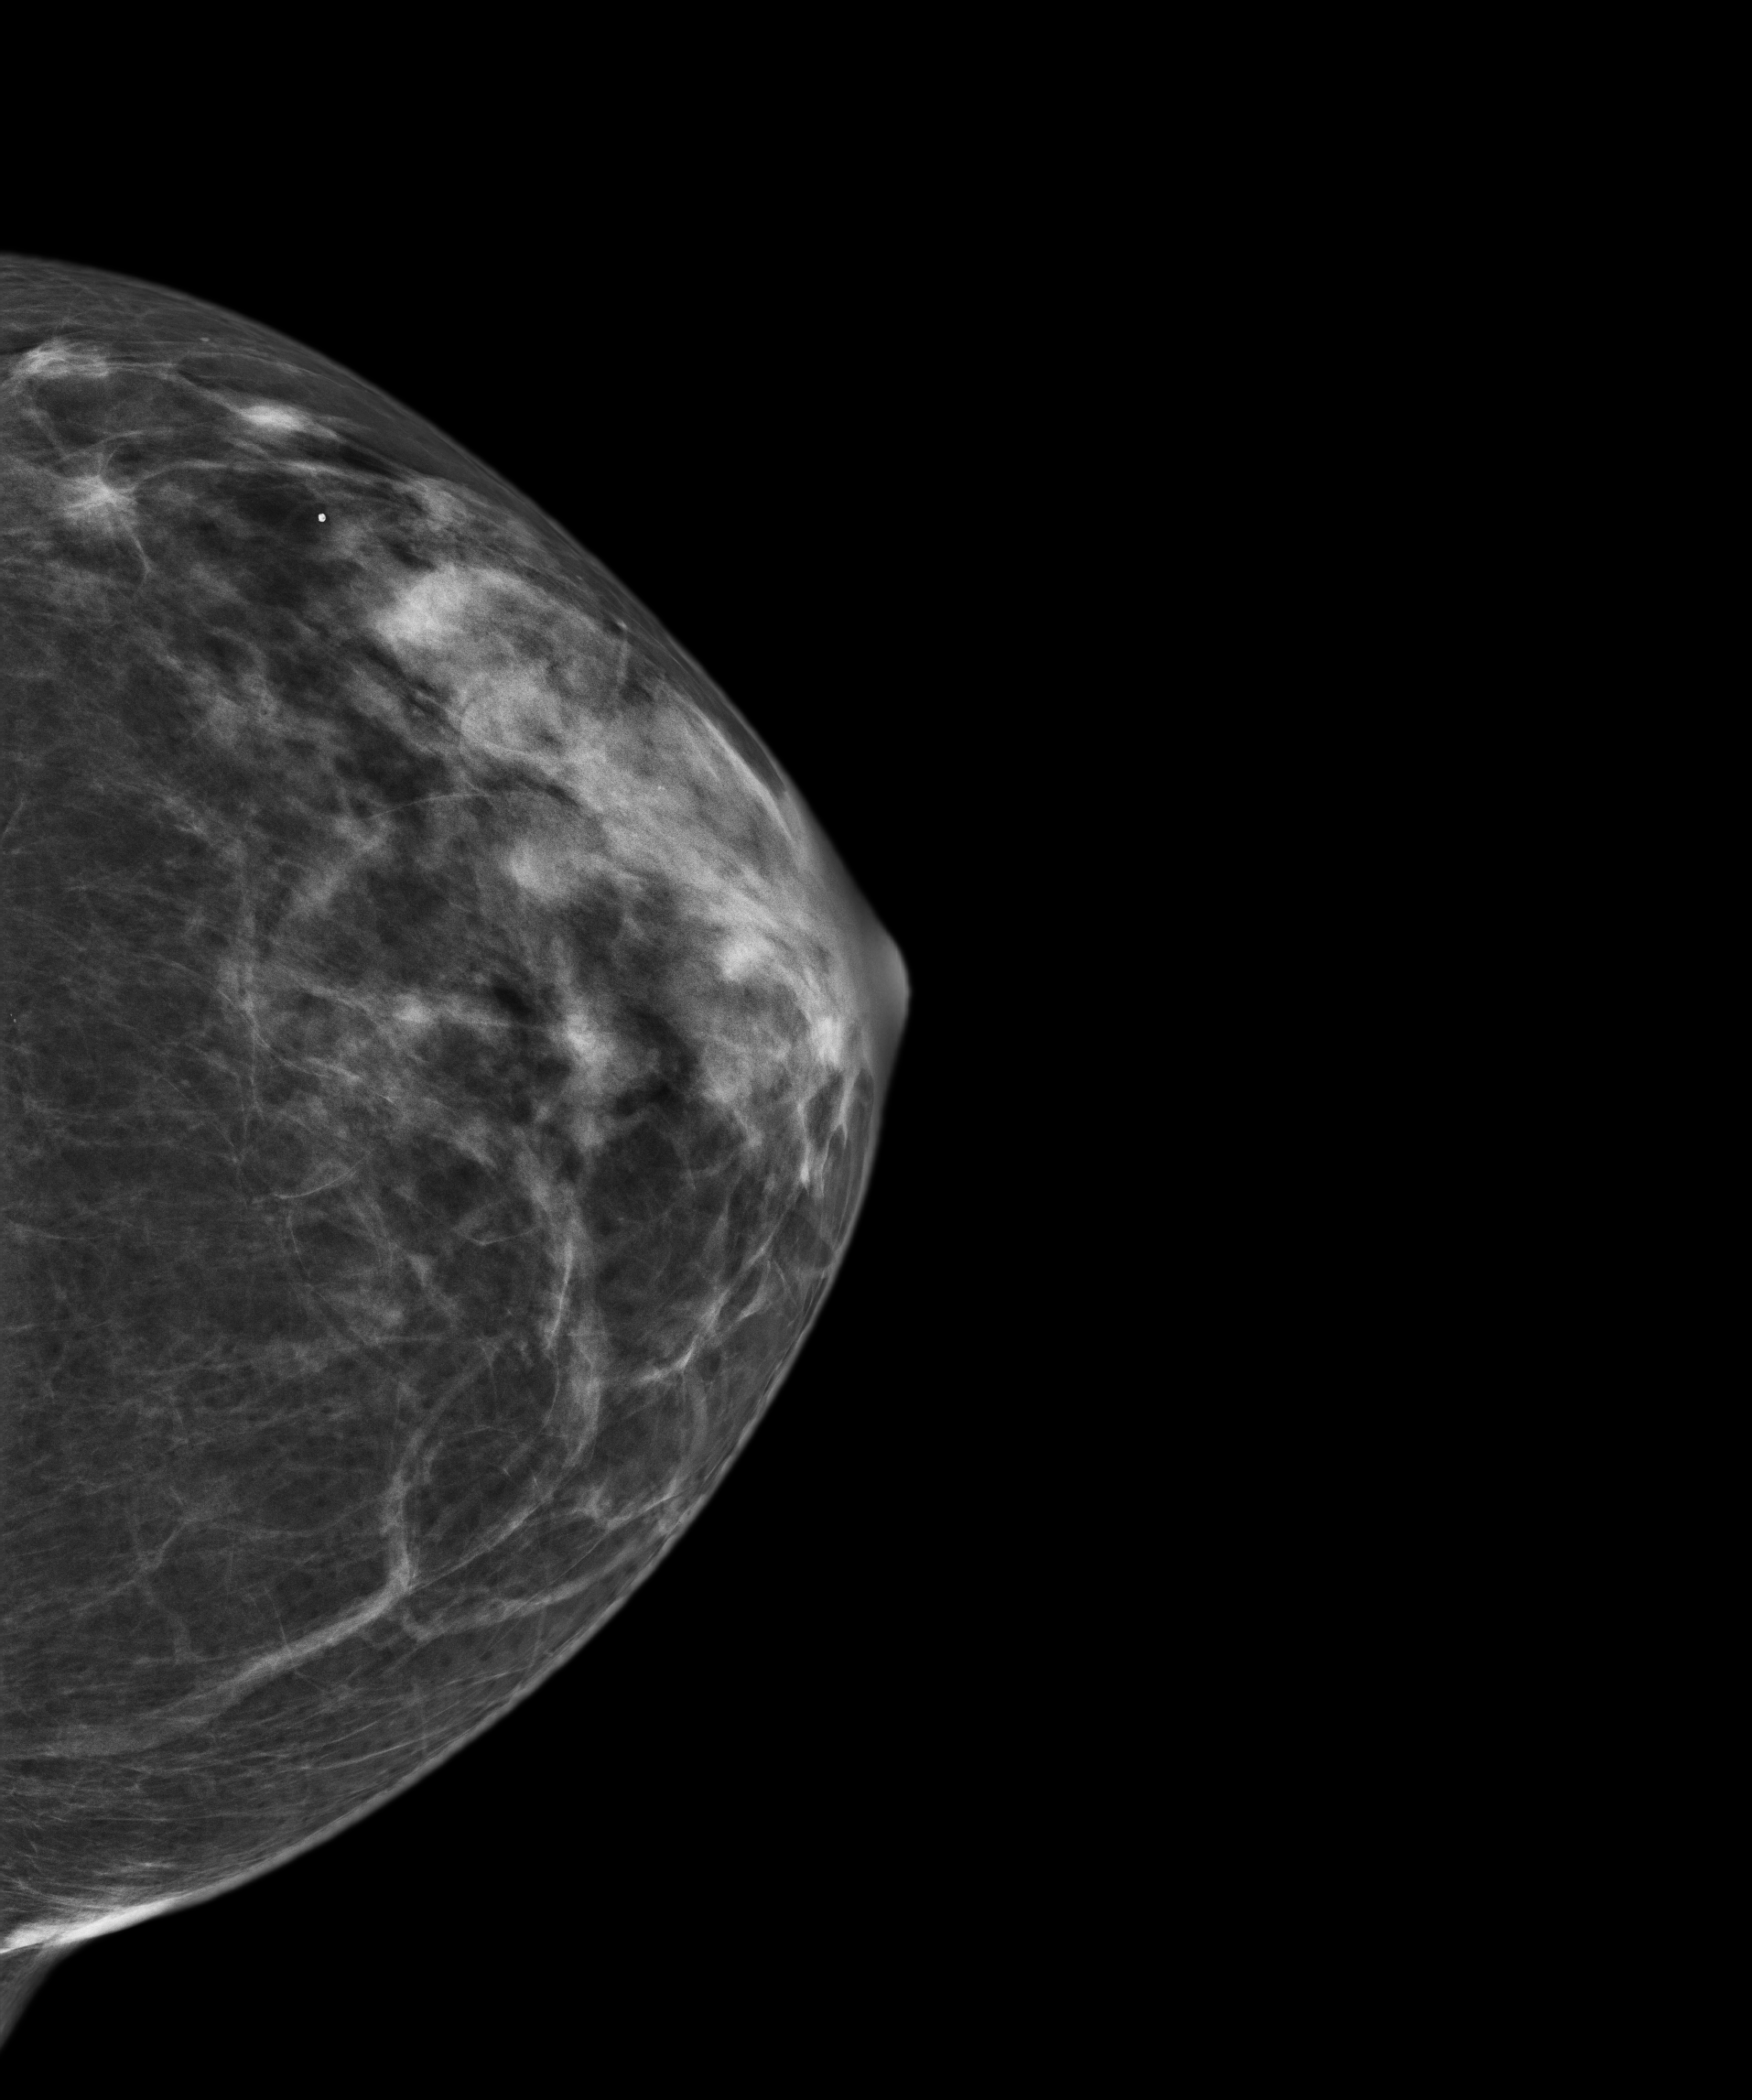
Digital mammogram (FFDM), left breast, craniocaudal (CC) view, annual screening mammography examination. Female patient, age 43 years.
- breast density at the screening exam (both breasts): heterogeneously dense (BI-RADS density category c)
- final BI-RADS assessment for this screening round (tomosynthesis exam, both breasts): category 1
- recall: no recall after this screen